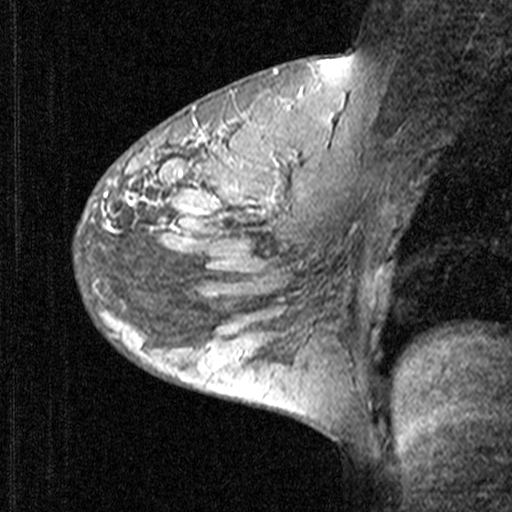
Breast MRI (dynamic contrast-enhanced), one sagittal slice; position 28 of 44 along the scan axis; dynamic contrast-enhanced study with each time point stored as its own series, time point 2 of 3 at this slice position (early post-contrast, ordered by acquisition time); 1.5 T; TE 4.5 ms, TR 11 ms; 3 mm slice thickness; 512 × 512 image matrix, field of view 200 × 200 mm. Patient: female, 27 years. Case-level facts recorded for this patient, not image findings: setting: breast cancer imaged before/during neoadjuvant chemotherapy; receptor status: HR-positive, HER2-negative.
Annotated regions visible in this slice (semi-automatic segmentation, software-assisted and operator-edited):
- analysis volume of interest (the breast-tissue region the enhancement analysis was run in; not a lesion): bounding box <74,146,165,239> (left, top, right, bottom; pixels)
- tumour enhancement mask (voxels above the 90 % enhancement threshold inside the analysis volume of interest): <139,197,164,220>